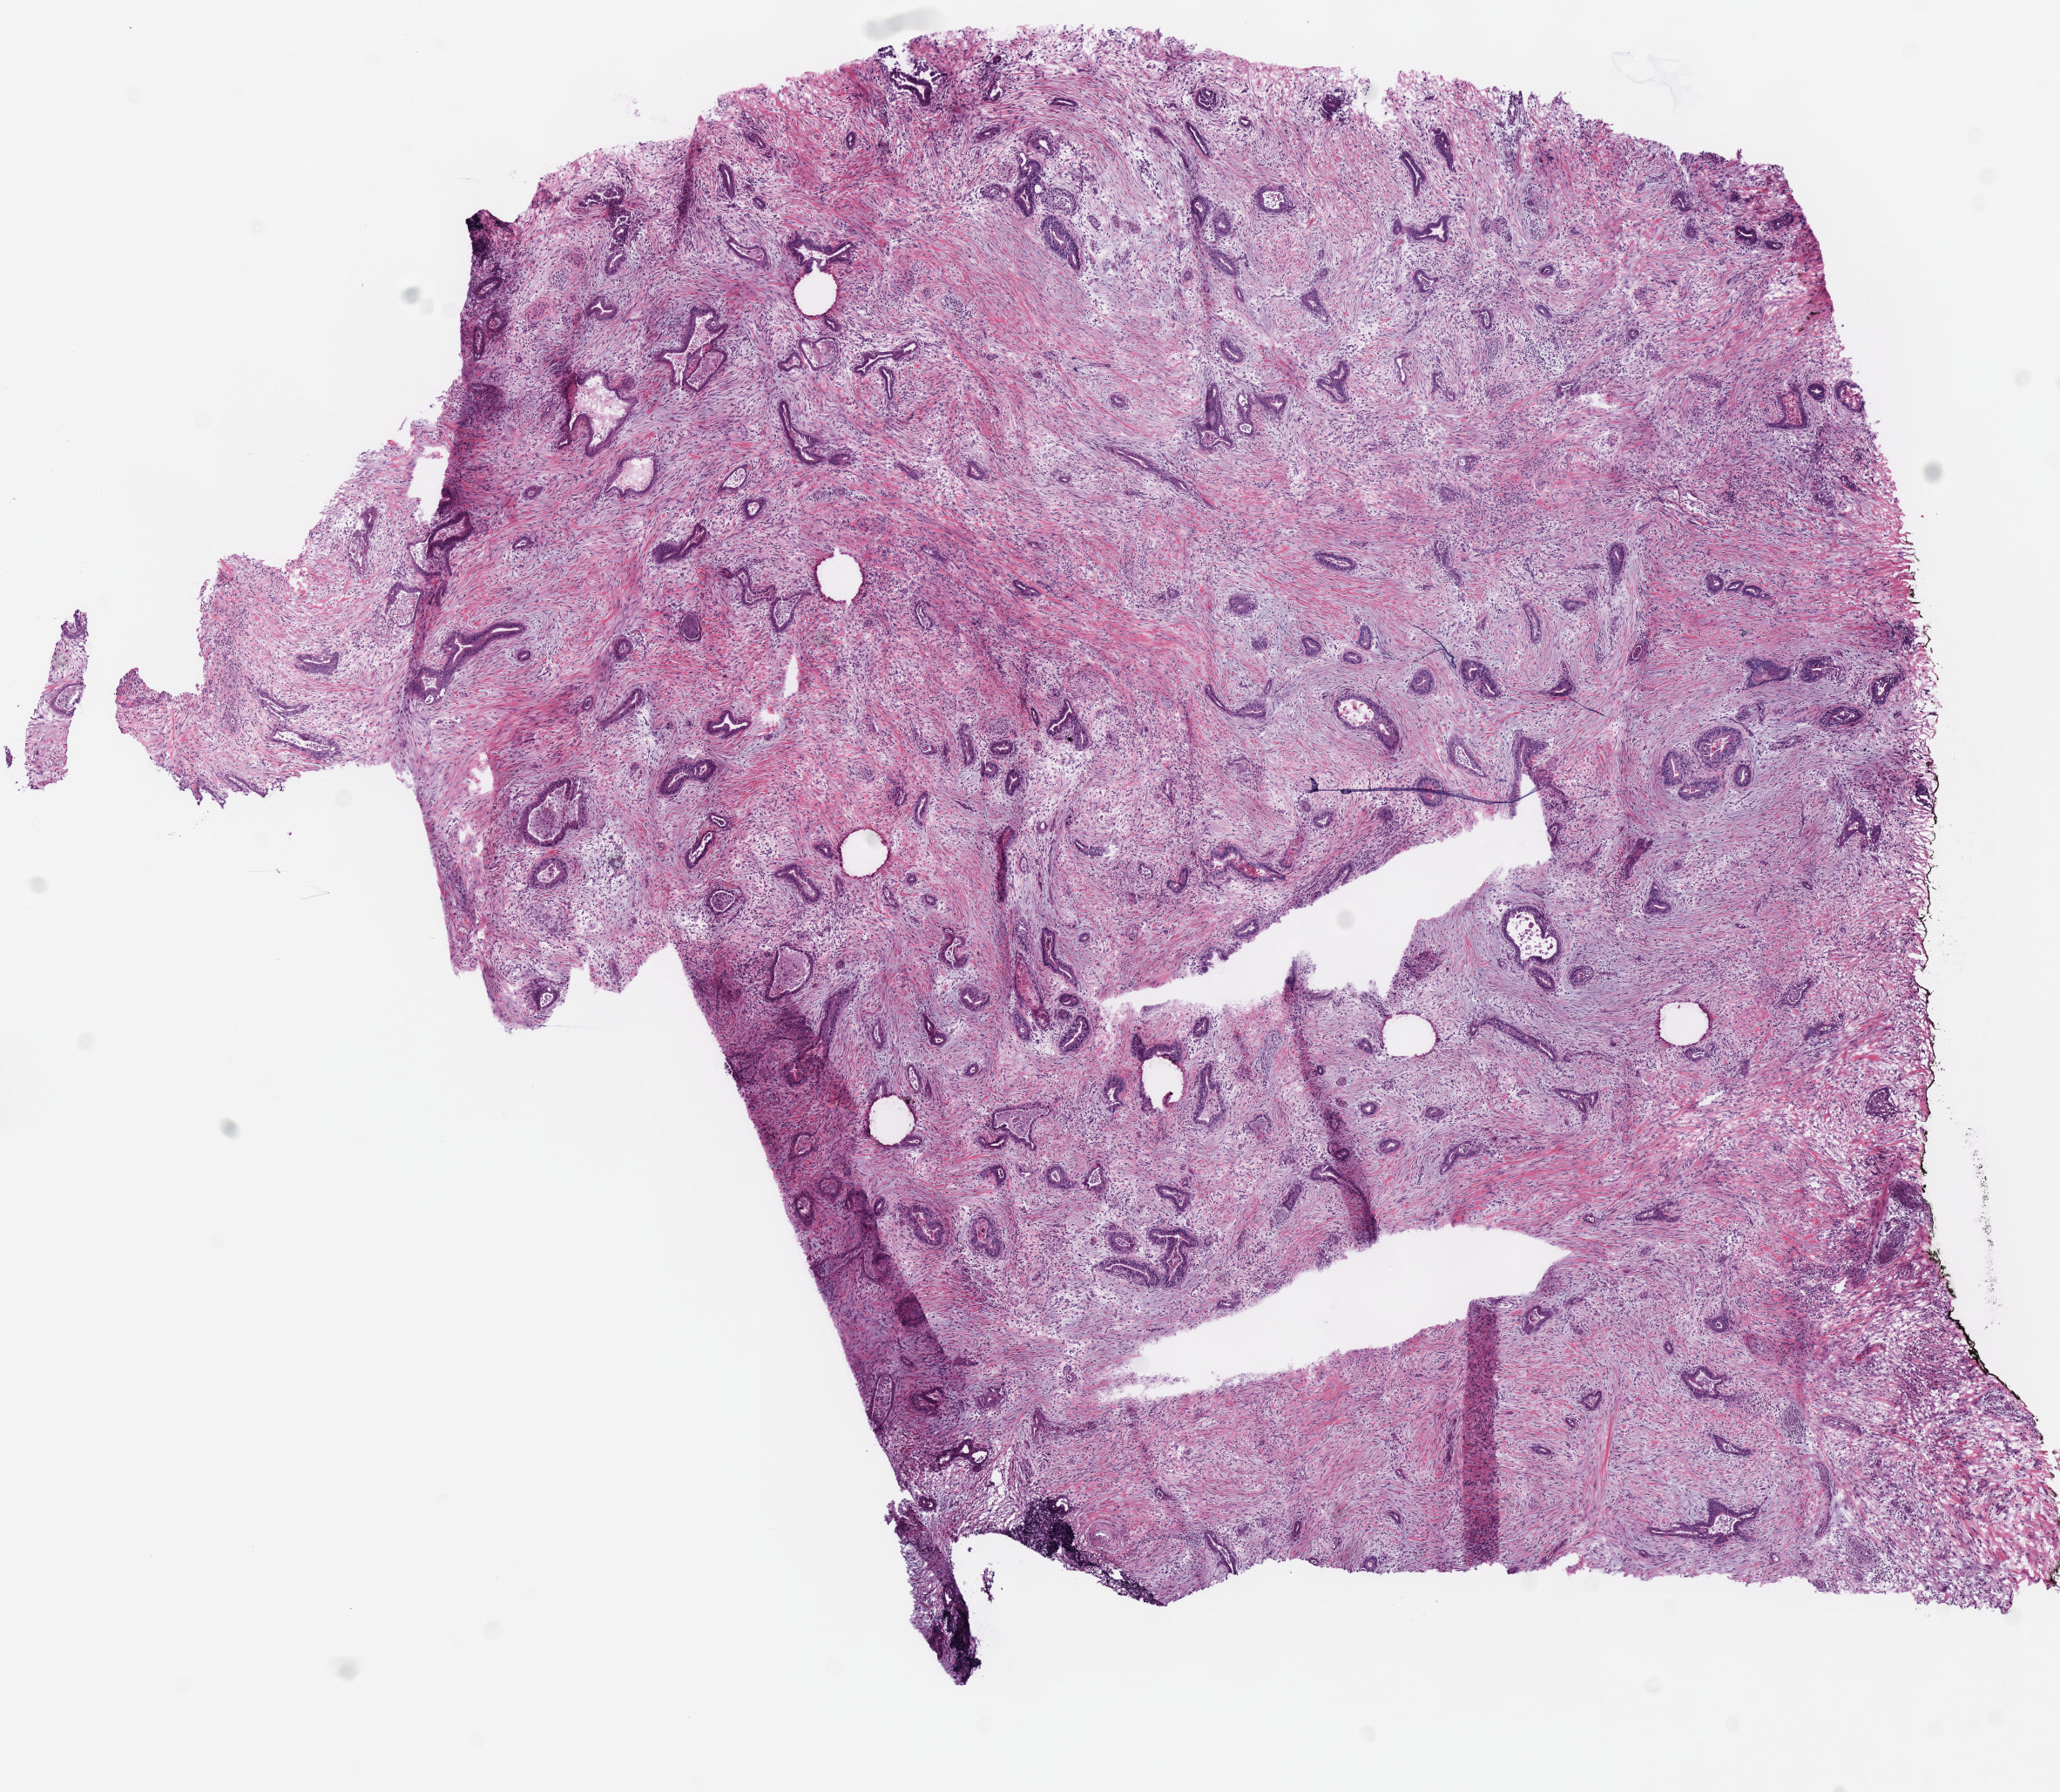
Digitized H&E-stained tissue section (whole slide) — whole scanned area (about 9.3 x 8.1 mm) shown as a low-resolution overview, frozen section from the bottom of the tissue portion, pancreas, primary tumour sample. Patient: male, age at initial diagnosis 66 years.
Histologic diagnosis: Infiltrating duct carcinoma, NOS (head of pancreas).